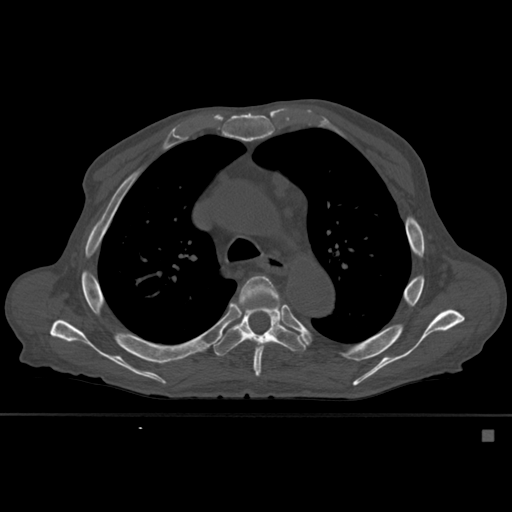
CT including the spine, one axial slice. Position 392 of 527 along the scan axis. Bone window (W 1800 / L 400 HU). 1.5 mm slice thickness. 512 × 512 image matrix. Male patient, age 78 years. Case-level facts recorded for this patient, not image findings: primary cancer: prostate.
Structures marked on this image (semi-automatically segmented with operator editing):
- T5 vertebra: box from (x=236, y=276) to (x=281, y=377) px
- T6 vertebra: (x=213, y=287)–(x=306, y=356)